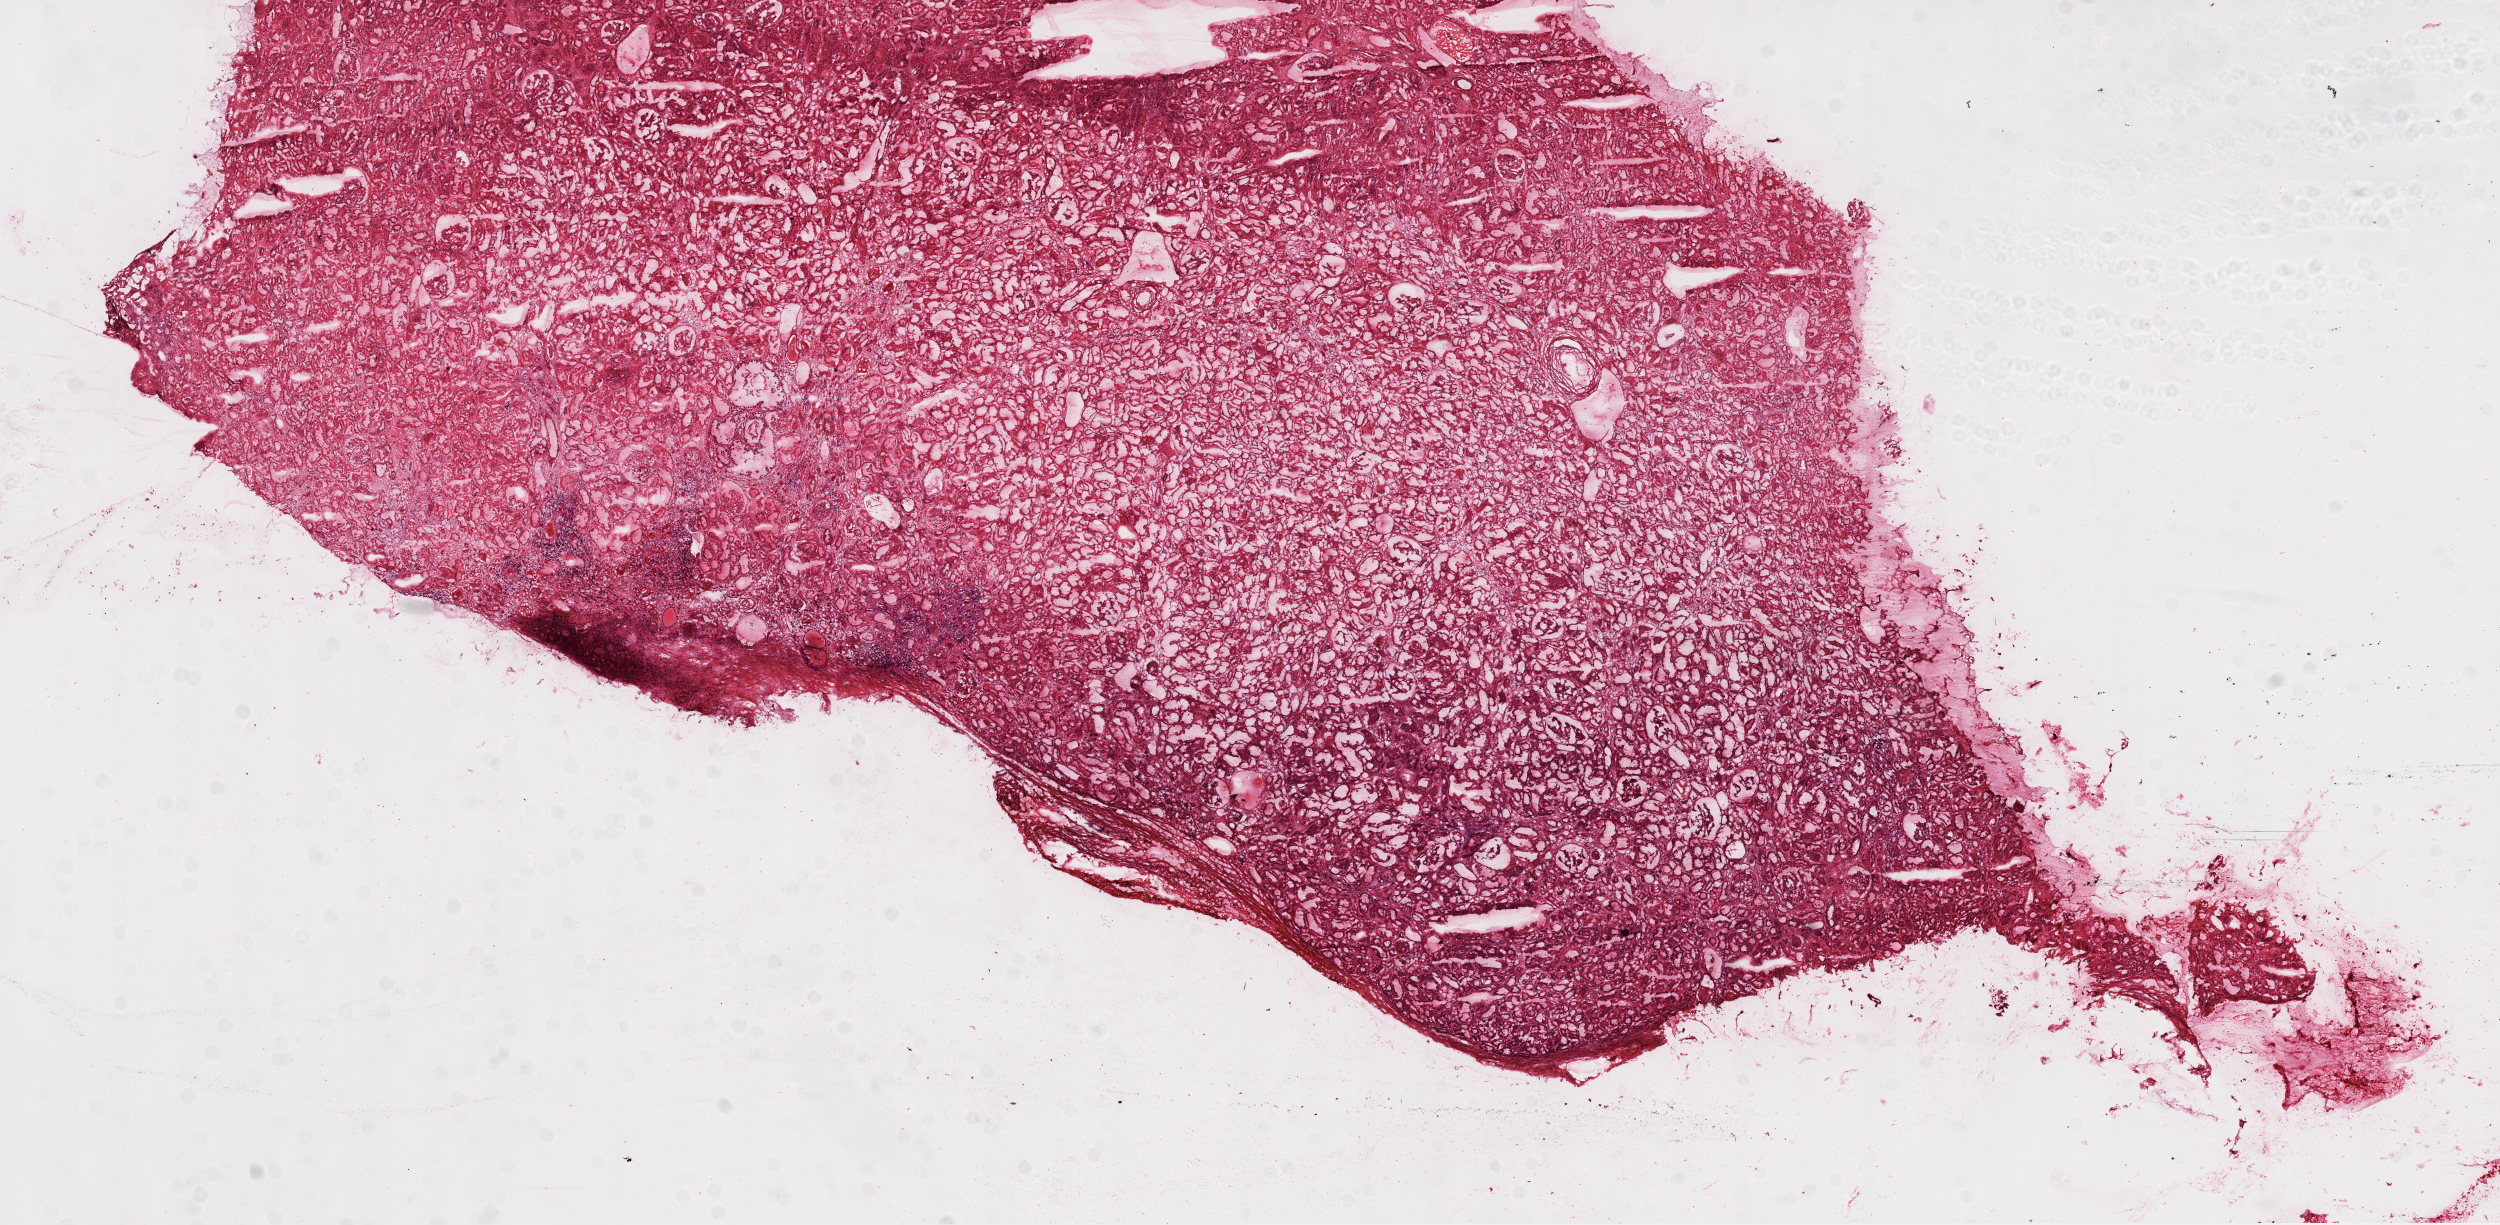
Whole-slide histology image, H&E-stained, whole scanned area (about 20.1 x 9.8 mm, acquisition: 20x scan) shown as a low-resolution overview, frozen section from the top of the tissue portion, kidney, solid tissue normal (non-tumour tissue) sample. Patient: female, age at initial diagnosis 75 years.
This section: solid tissue normal (non-tumour) sample from the same patient. Patient diagnosis: Clear cell adenocarcinoma, NOS.